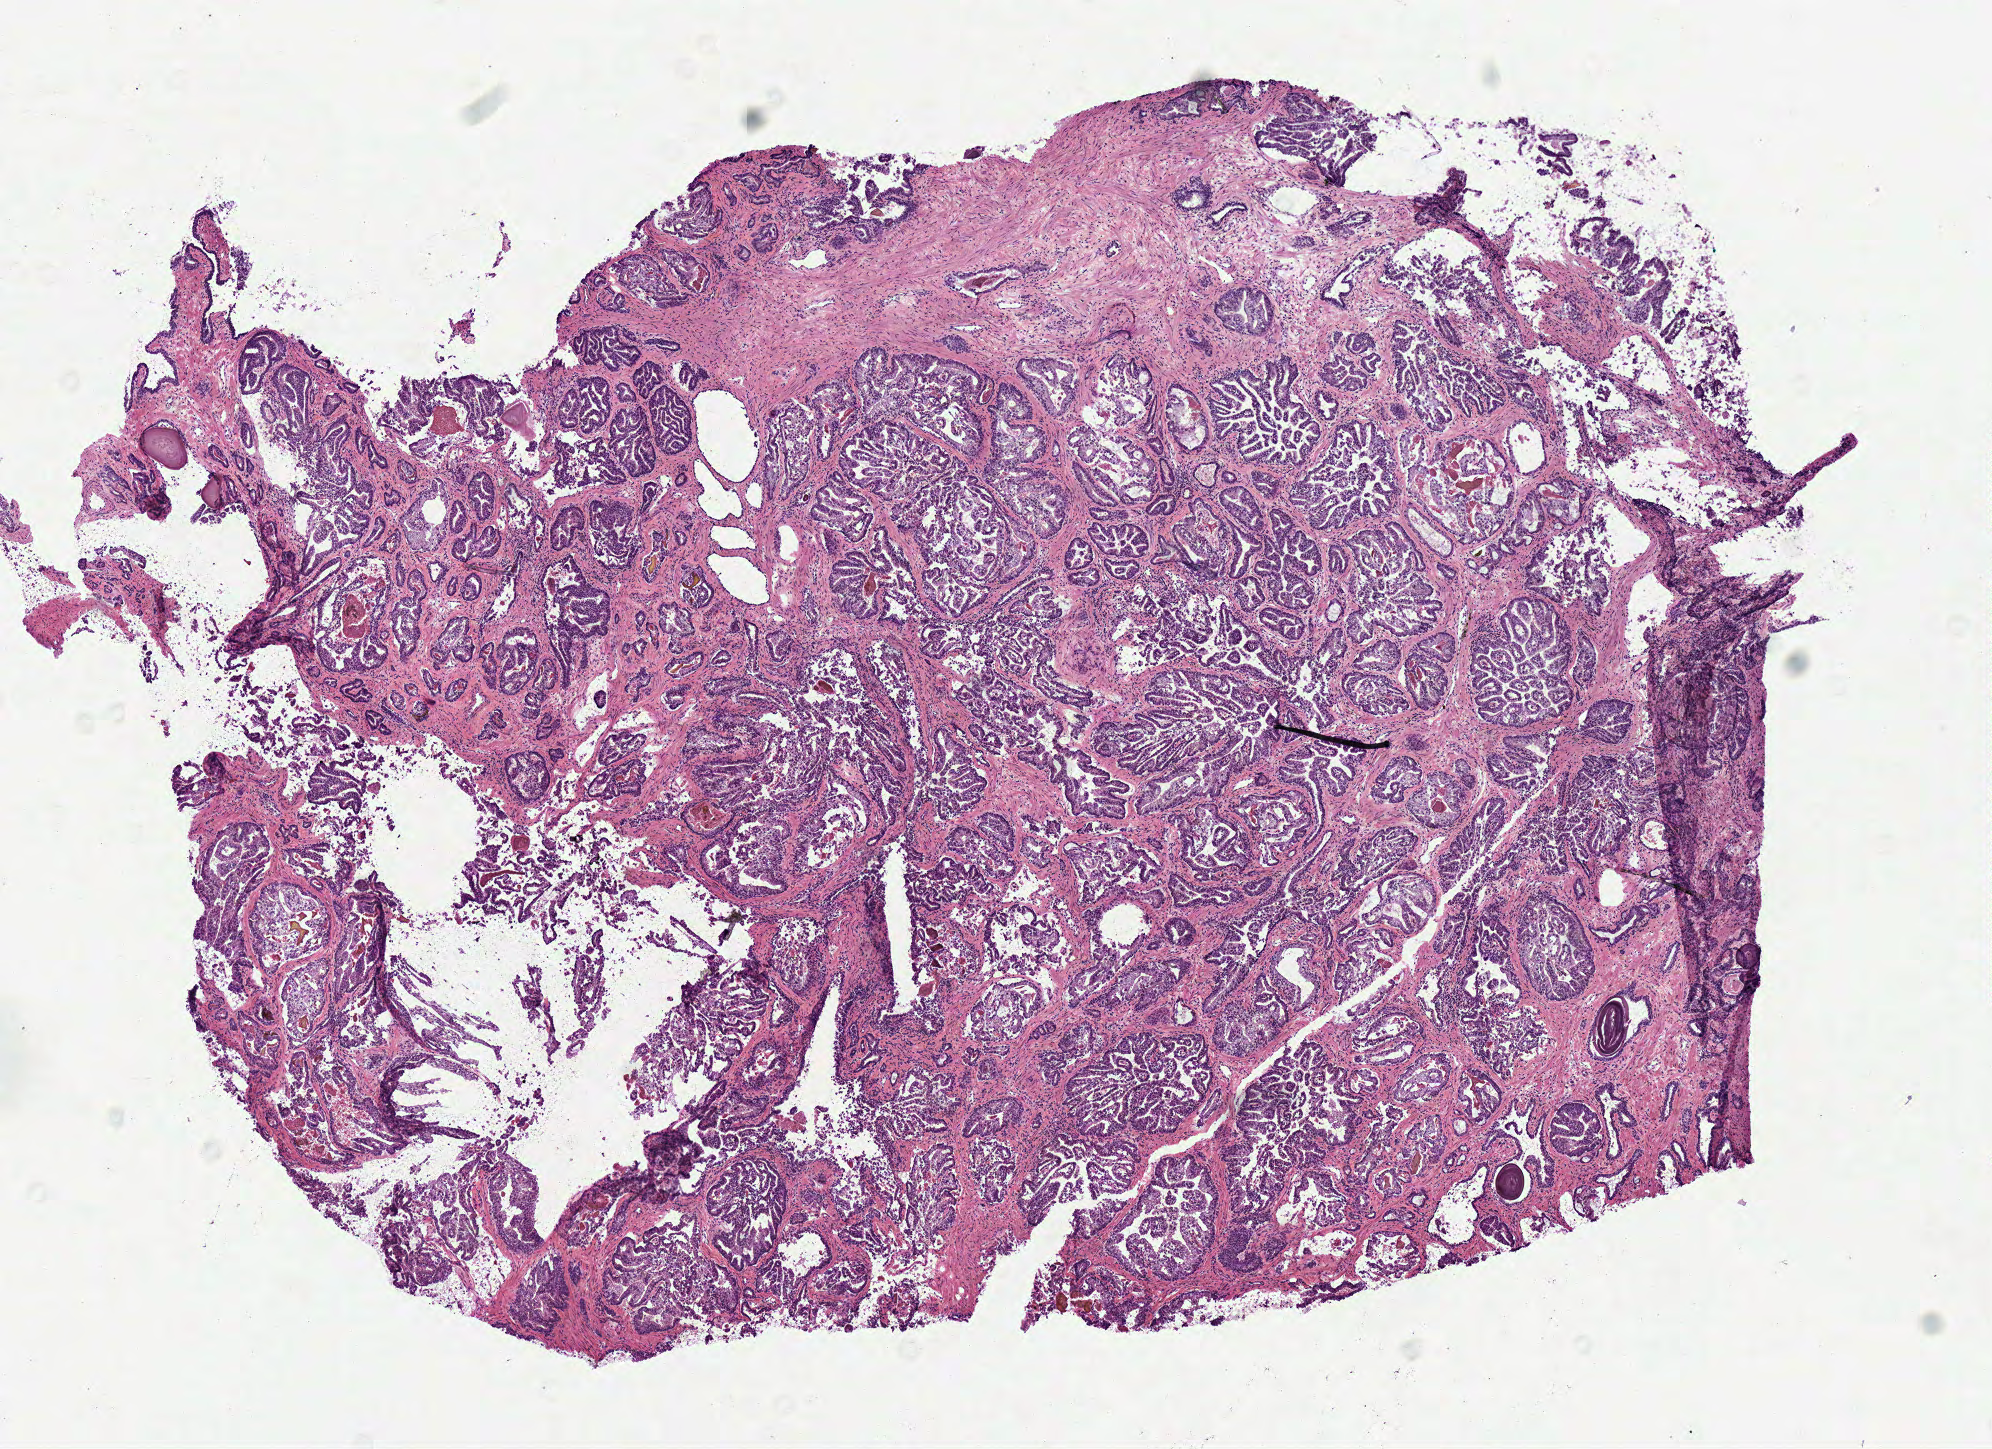
Whole-slide histology image, H&E, low-resolution overview of the scanned area, about 7.8 x 5.7 mm; frozen section from the top of the tissue portion; prostate, primary tumour sample. Male, age 61 years at initial diagnosis. Gleason score: 6 (3+3). Slide review estimates, as recorded: tumour cells 65%, tumour nuclei 75%, normal cells 20%, stromal cells 10%, necrosis 5%. Infiltration values recorded for this section: lymphocyte infiltration 3%, monocyte infiltration 2%, neutrophil infiltration 0%.
Histologic diagnosis: Acinar cell carcinoma (prostate gland). Laterality: bilateral.